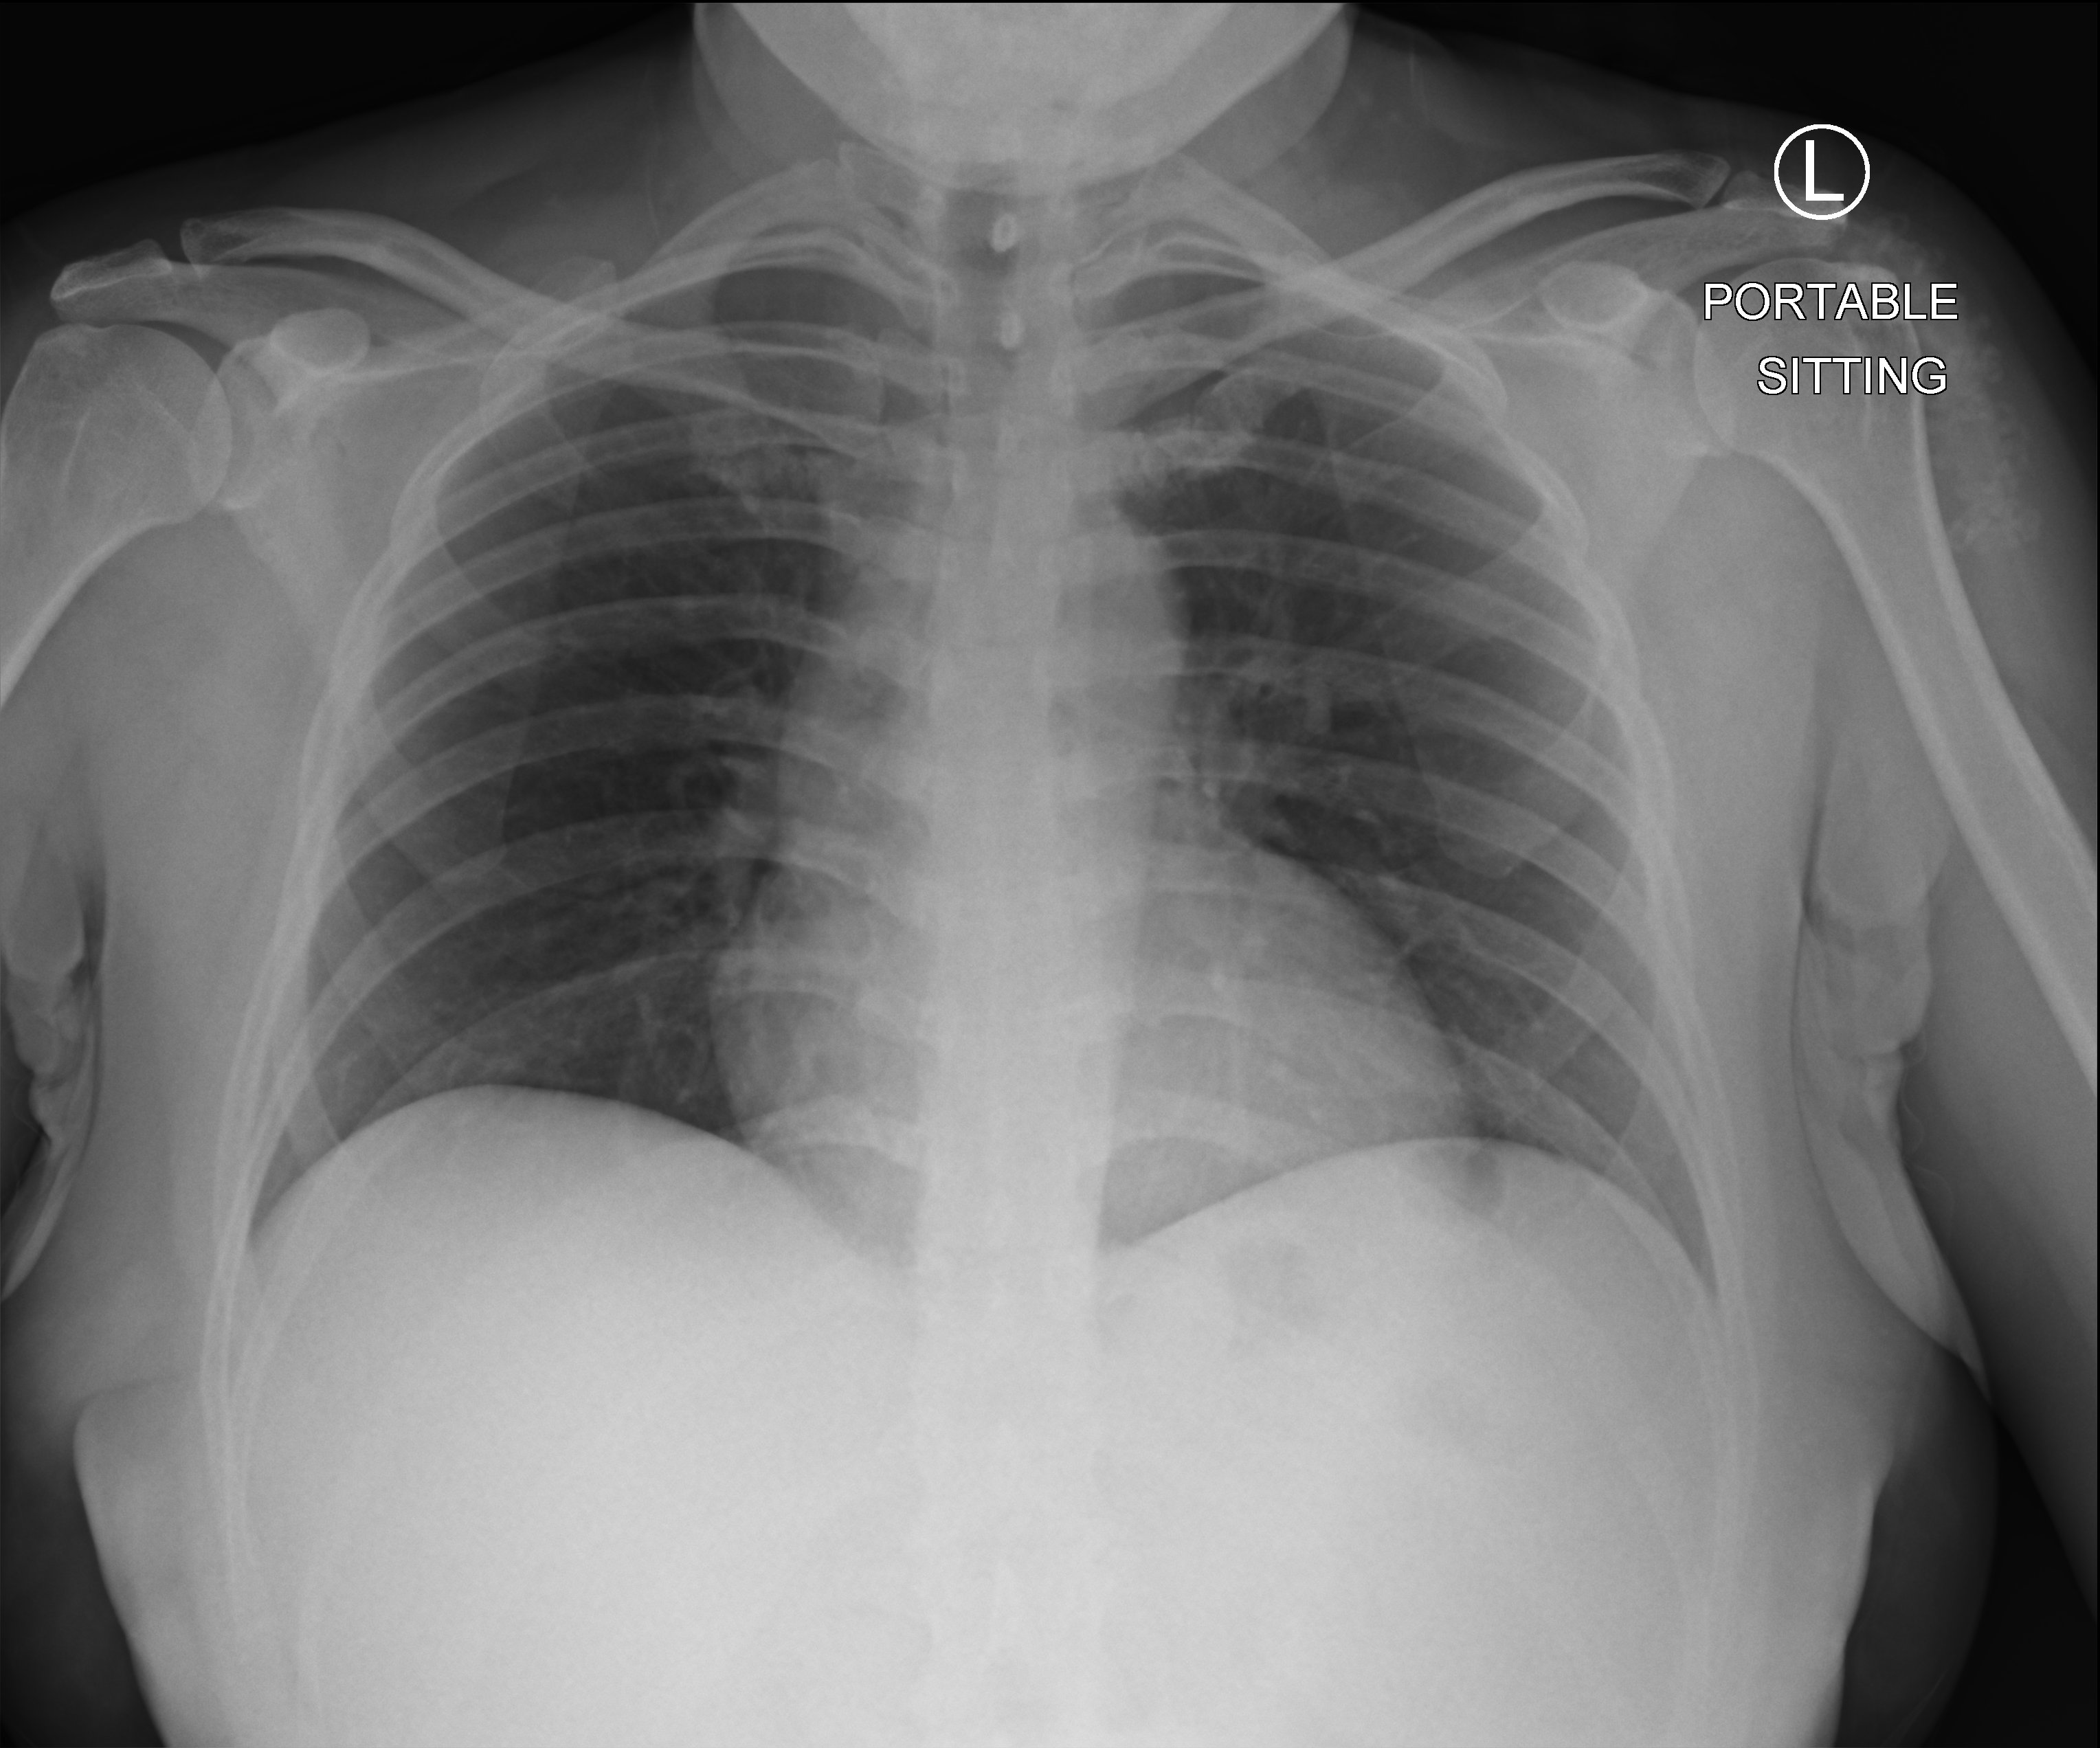
Bedside chest radiograph (computed radiography), anteroposterior (AP) projection. Patient hospitalised with COVID-19; female, aged 18–59 years.
From the hospital-stay record, not from the radiograph (when in the stay this image was taken is not recorded):
- length of hospital stay: 1 day
- mechanically ventilated during this hospital stay: no